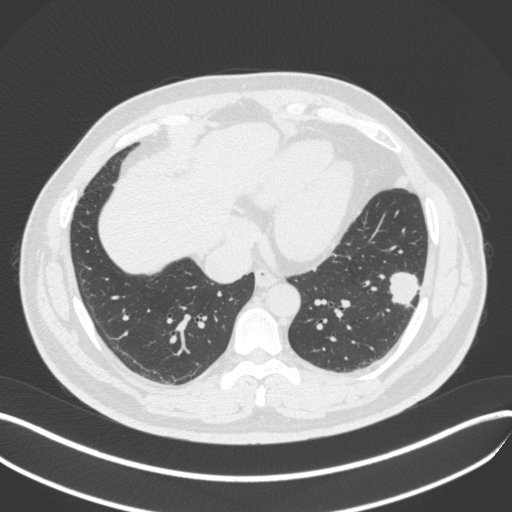
Chest CT, one axial slice; position 137 of 420 along the scan axis; reconstruction kernel B31f; 120 kVp; lung window (W 1500 / L -600 HU); 1 mm slice thickness; 512 × 512 image matrix, field of view 400 × 400 mm. Patient: male, 39 years. From the clinical record (not read from this slice): clinical TNM (as recorded): T2a N0 M0.
Outlined on this slice (rectangle marked by the reading radiologist):
- lung tumour (recorded histology: adenocarcinoma): bounding box [x1, y1, x2, y2] px = [384, 266, 428, 311]